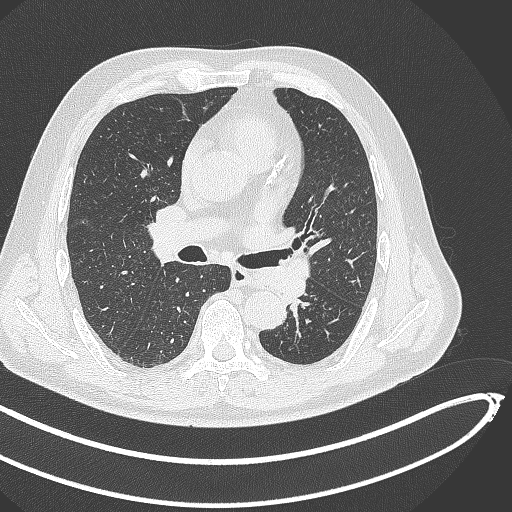
Chest CT, one axial slice. Position 264 of 468 along the scan axis. Reconstruction kernel B70f. Lung window (W 1500 / L -600 HU). 1 mm slice thickness. 512 × 512 image matrix. Patient: male, 64 years. Case-level facts recorded for this patient, not image findings: clinical TNM (as recorded): T1c N0 M0.
Outlined on this slice (bounding box drawn by a radiologist):
- lung tumour (recorded histology: squamous cell carcinoma): bounding box [x1, y1, x2, y2] px = [264, 255, 312, 306]